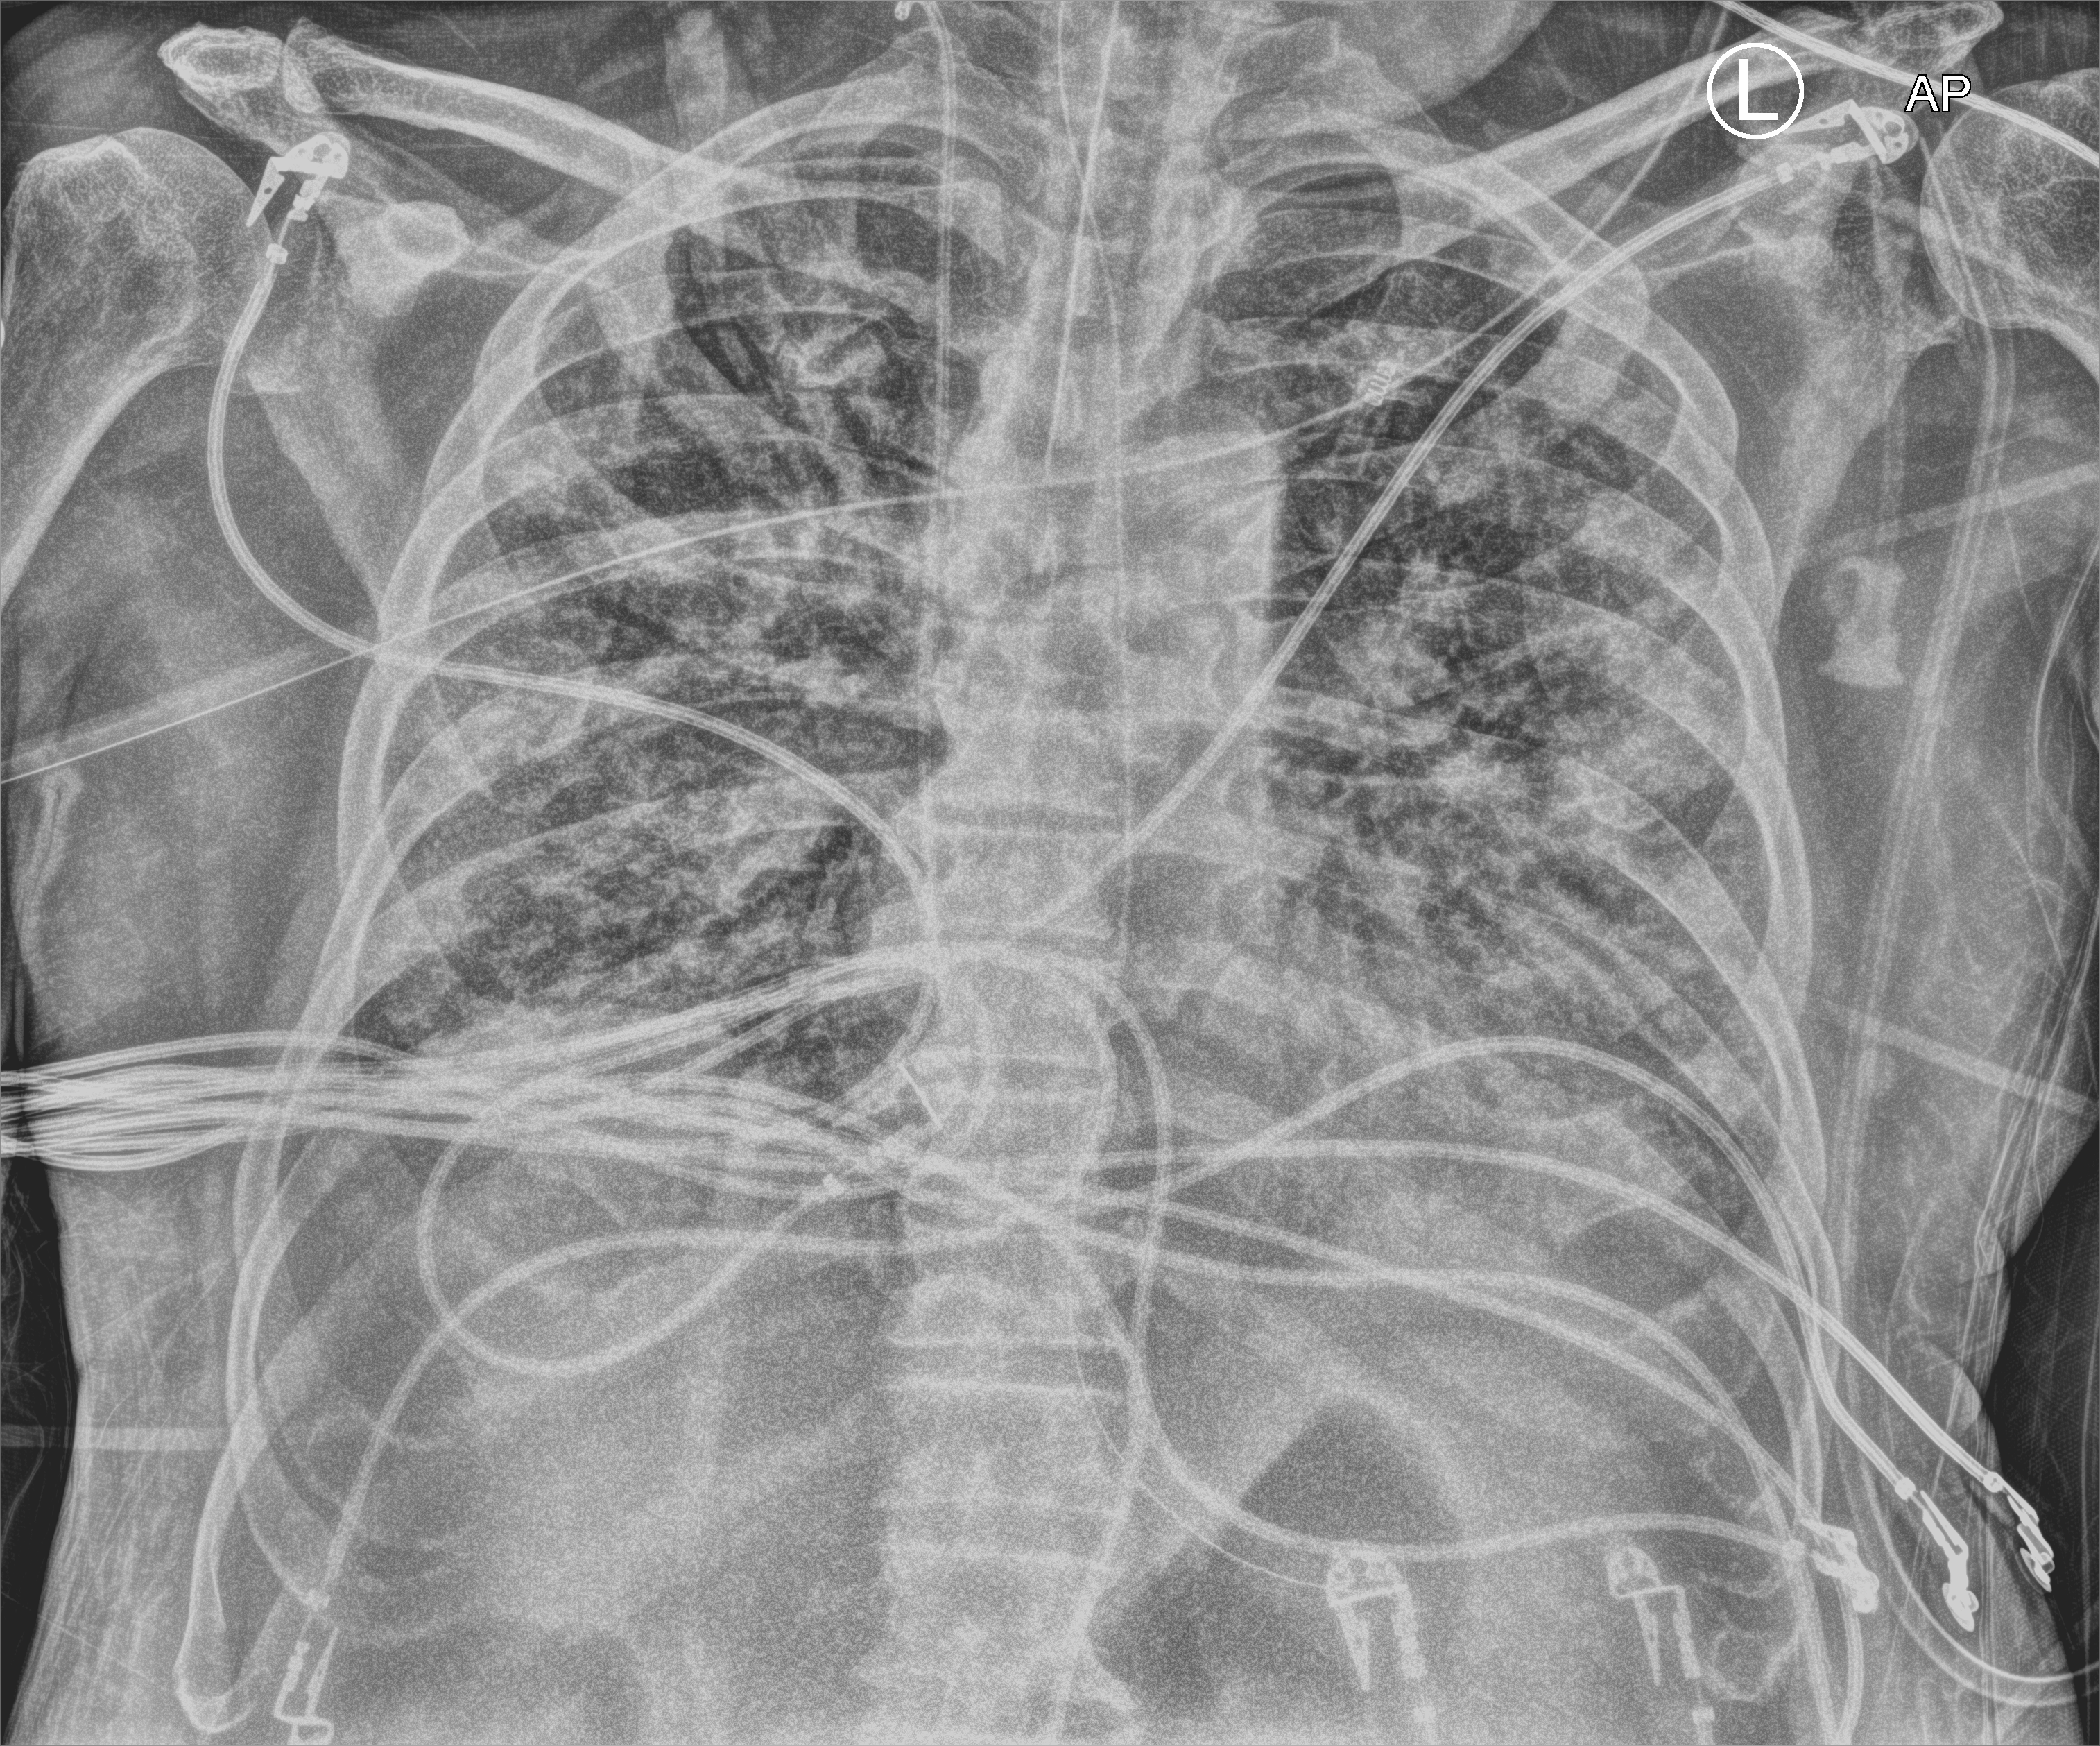
Portable chest radiograph, anteroposterior (AP) projection. Male patient hospitalised with COVID-19, age 75–90 years.
Admission-level facts for this patient (not findings on this image; timing relative to this image not recorded):
- length of hospital stay: 33 days
- mechanically ventilated during this hospital stay: yes